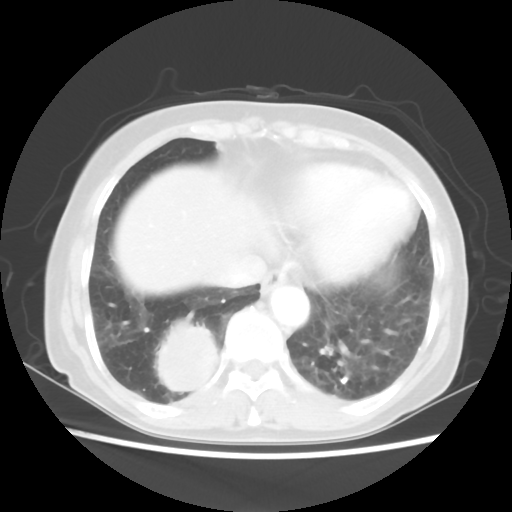
Chest CT, one axial slice. Slice 18 of 56 in the series (ordered by position). Reconstruction kernel STANDARD. Lung window (W 1500 / L -600 HU). 512 × 512 image matrix, field of view 332 × 332 mm. Female patient, age 66 years. Case-level facts recorded for this patient, not image findings: clinical TNM (as recorded): T2 N3 M0; histopathological grade: G3.
Outlined on this slice (rectangle marked by the reading radiologist):
- lung tumour (recorded histology: small cell carcinoma): bounding box [x1, y1, x2, y2] px = [150, 317, 247, 436]